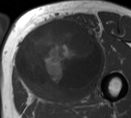
MRI of an extremity soft-tissue mass, one axial slice; position 39 of 55 along the scan axis; MR volume resampled by the dataset authors to the PET/CT grid (not the native acquisition matrix); 3.27 mm slice thickness; 131 × 118 image matrix, field of view 128 × 115 mm. Male patient. From the clinical record (not read from this slice): histological type: pleiomorphic liposarcoma; grade: high; site of the primary tumour: left thigh.
Outlined on this slice (expert contour drawn on MRI and transferred to this co-registered scan by the dataset authors):
- gross tumour volume including surrounding oedema: box from (x=16, y=18) to (x=104, y=97) px
- gross tumour volume (mass): (x=16, y=18)–(x=101, y=97)